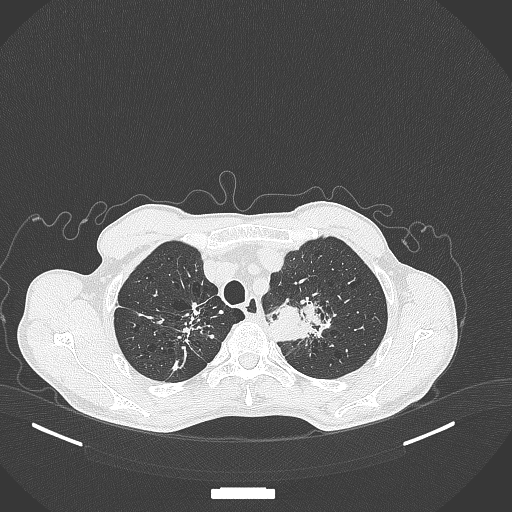
Chest CT, one axial slice. Reconstruction kernel B70f. 120 kVp. Lung window (W 1500 / L -600 HU). 512 × 512 image matrix, field of view 400 × 400 mm. Male patient, age 65 years. From the clinical record (not read from this slice): clinical TNM (as recorded): T2b N0 M0; histopathological grade: G2.
Structures marked on this image (rectangle marked by the reading radiologist):
- lung tumour (recorded histology: adenocarcinoma): bounding box <265,286,333,348> (left, top, right, bottom; pixels)